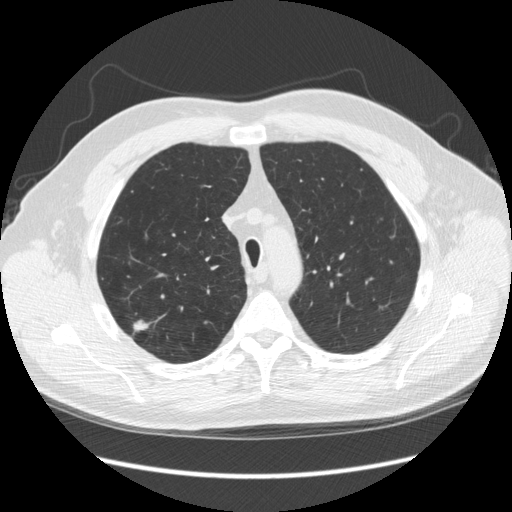
Chest CT (low-dose screening protocol), one axial image. Third annual screen. Lung window (W 1500 / L -600 HU). 2.5 mm slice thickness. Standard (soft-tissue) reconstruction kernel (STANDARD). 120 kVp. Slice 57 of 248 in the series. 512 × 512 image matrix. Male, age 64 years at enrolment.
Expert reader's lesion annotation, box from (x=118, y=313) to (x=167, y=354) px. The screening reader recorded 4 non-calcified nodules or masses ≥4 mm on this exam (right upper lobe, right upper lobe, right upper lobe, right upper lobe); which of them this box marks is not recorded. Official screen result: positive, other. Participant outcome: lung cancer diagnosed 15 days after this screen — adenocarcinoma, NOS, right upper lobe, moderately differentiated (G2), stage IA (AJCC 6th edition), 14 mm at pathology.